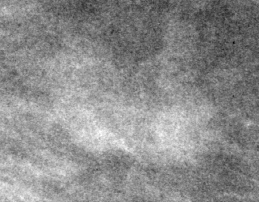
Cropped region of a digitized screen-film mammogram centred on a radiologist-marked abnormality, left breast, MLO view.
- Mass, shape lymph node, margins circumscribed; BI-RADS assessment category 3; subtlety rating 2 on a 1 (subtle) to 5 (obvious) scale; benign; no additional work-up was recommended (benign without callback).